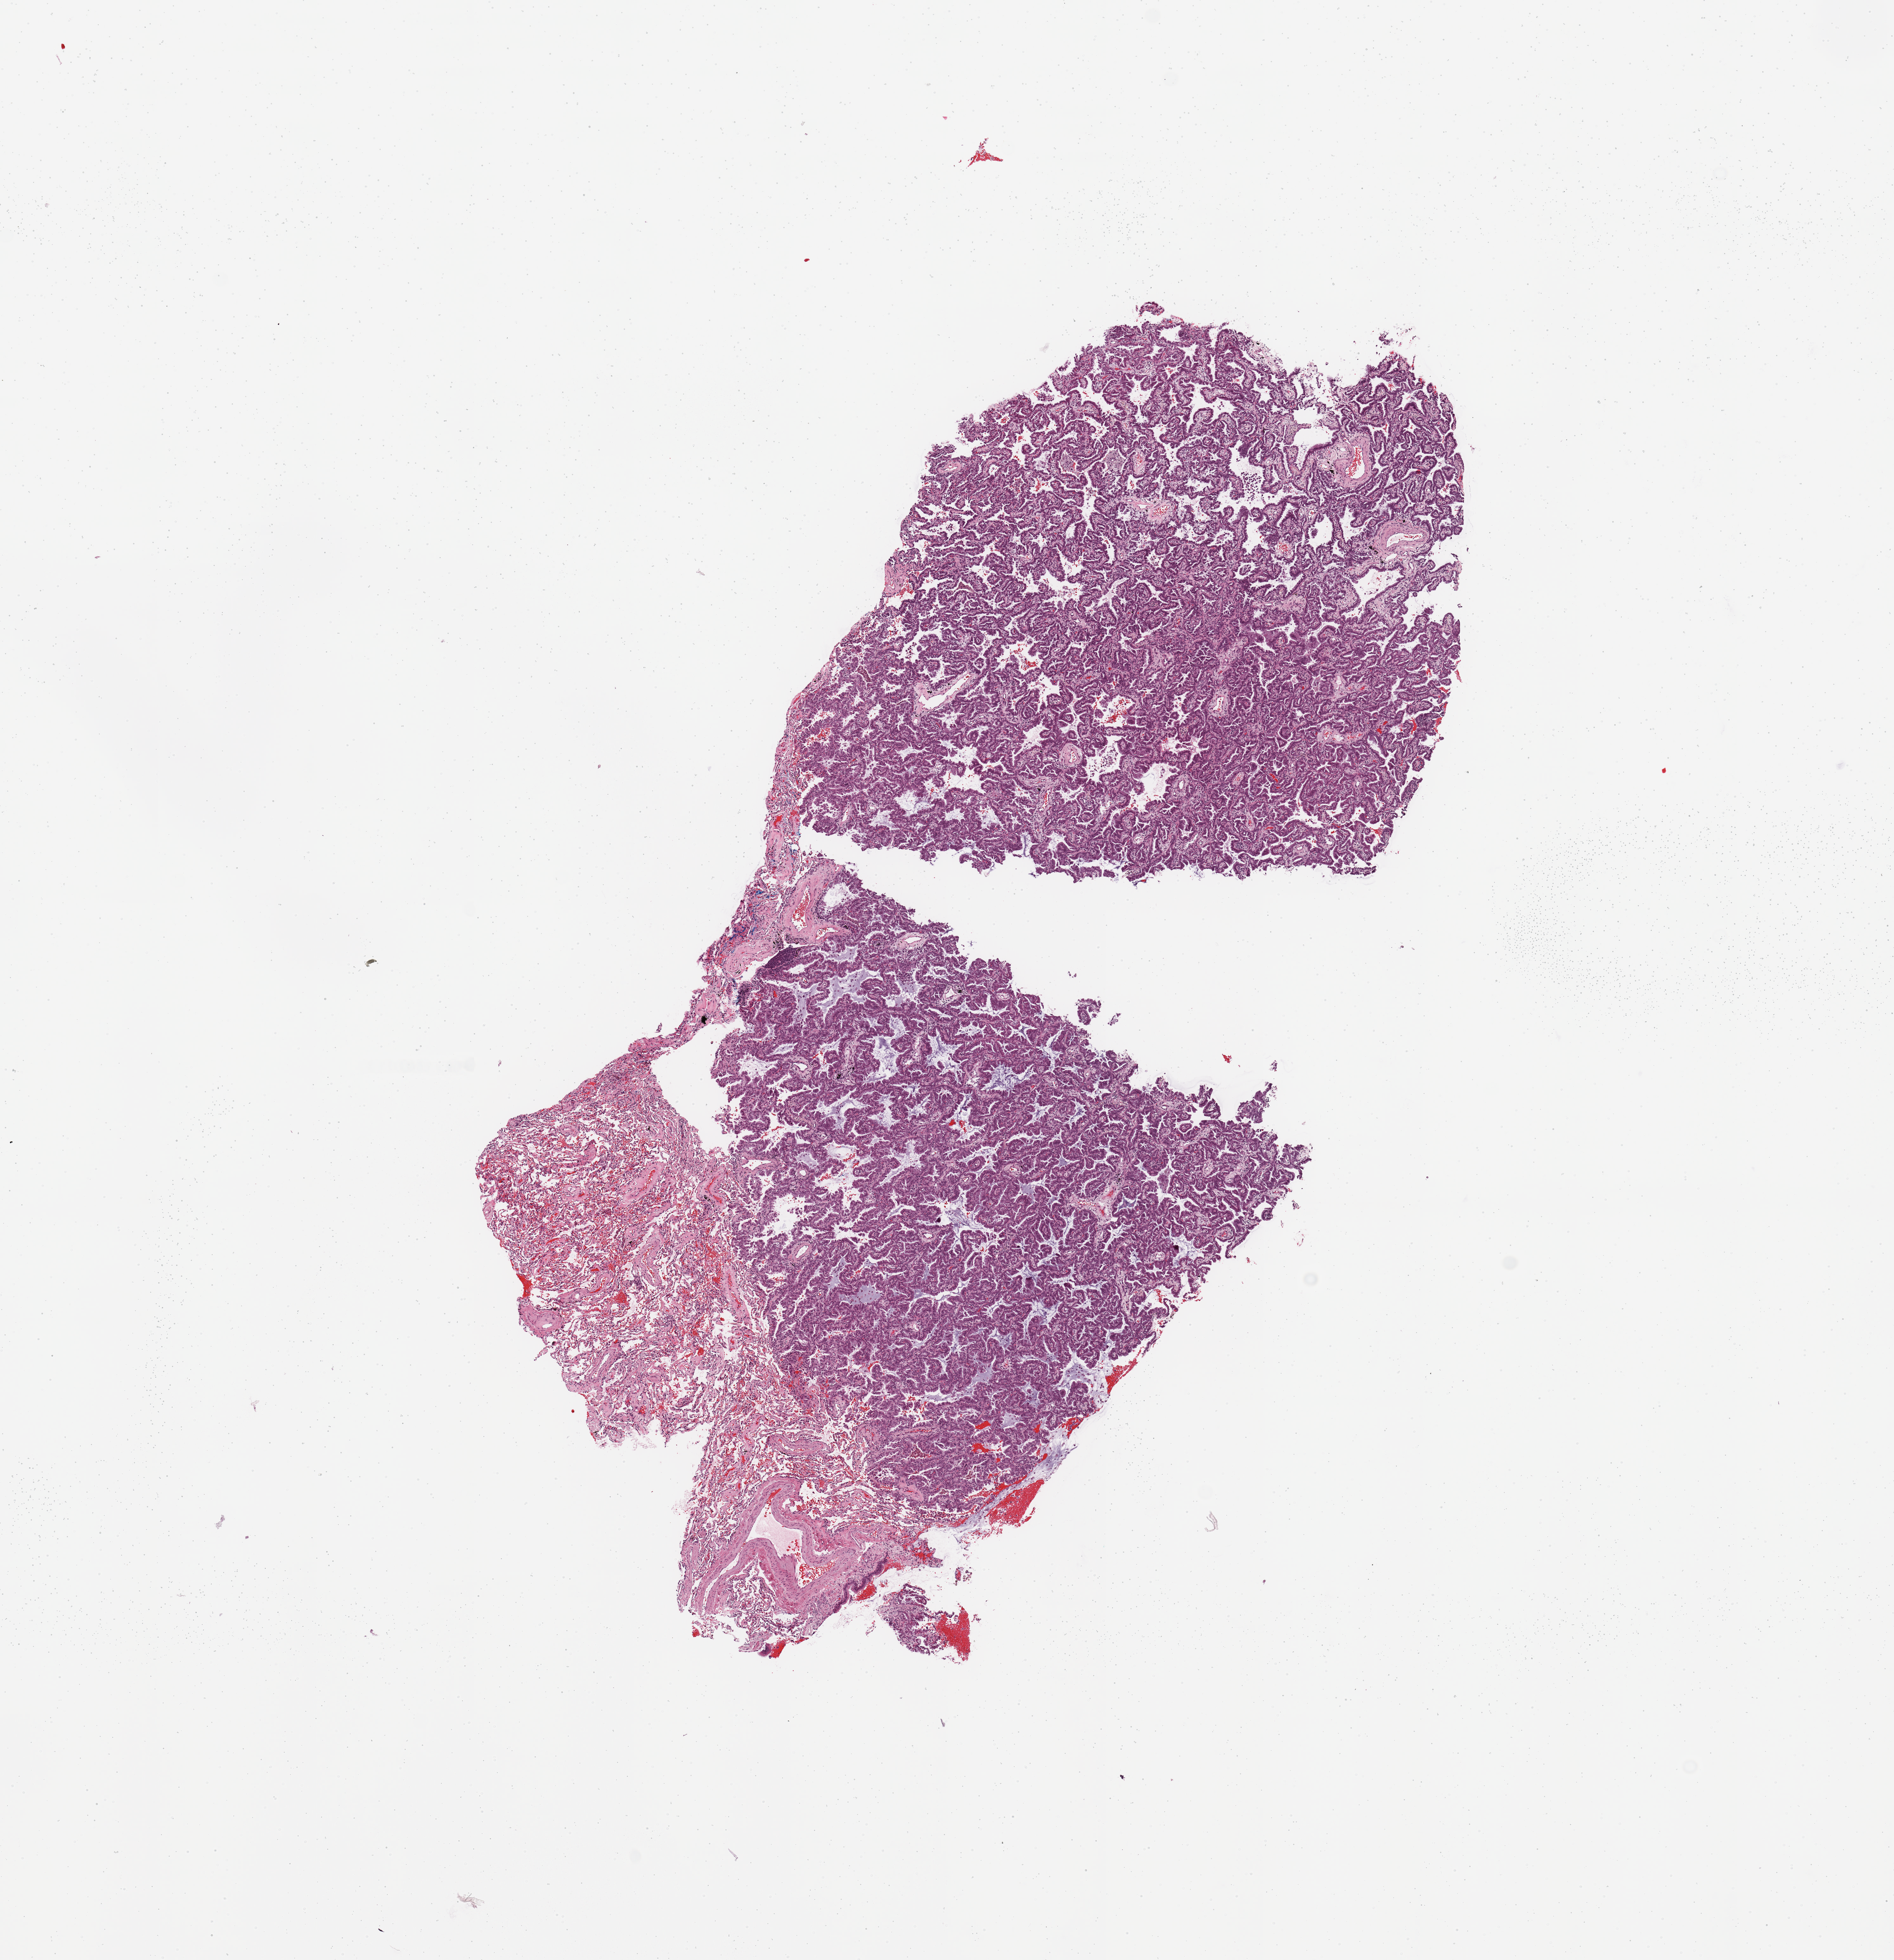
Hematoxylin and eosin (H&E) stained whole-slide image — shown as a low-resolution overview of the whole scanned area (about 11.8 x 12.2 mm, from a 20x scan). Tumour tissue sample, sampled site: lung. 71-year-old female patient. Histologic grade: G2 (moderately differentiated). Slide review estimates, as recorded: tumour nuclei 80%, necrosis 0%.
Primary tumour site (as recorded): right upper lobe. AJCC pathologic stage: IB. Histologic diagnosis: Adenocarcinoma, NOS.